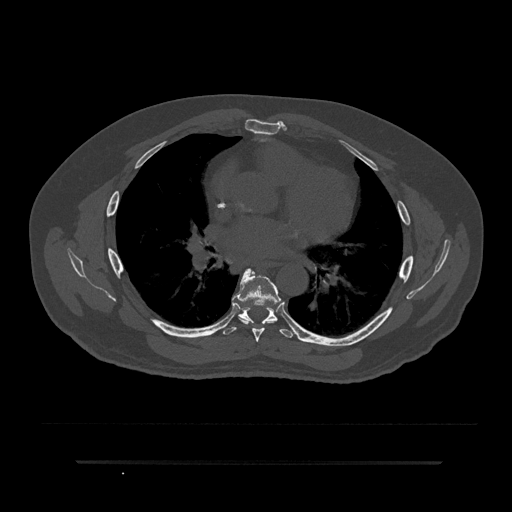
CT including the spine, one axial slice; slice 506 of 797 in the series (ordered by position); reconstruction kernel Br40s/3; 120 kVp; bone window (W 1800 / L 400 HU); 0.5 mm slice thickness; 512 × 512 image matrix, field of view 464 × 464 mm. Male patient, age 59 years. Case-level facts recorded for this patient, not image findings: primary cancer: bile ducts.
Structures marked on this image (semi-automatic segmentation, software-assisted and operator-edited):
- T6 vertebra: bounding box <232,268,281,342> (left, top, right, bottom; pixels)
- T7 vertebra: <223,306,295,338>